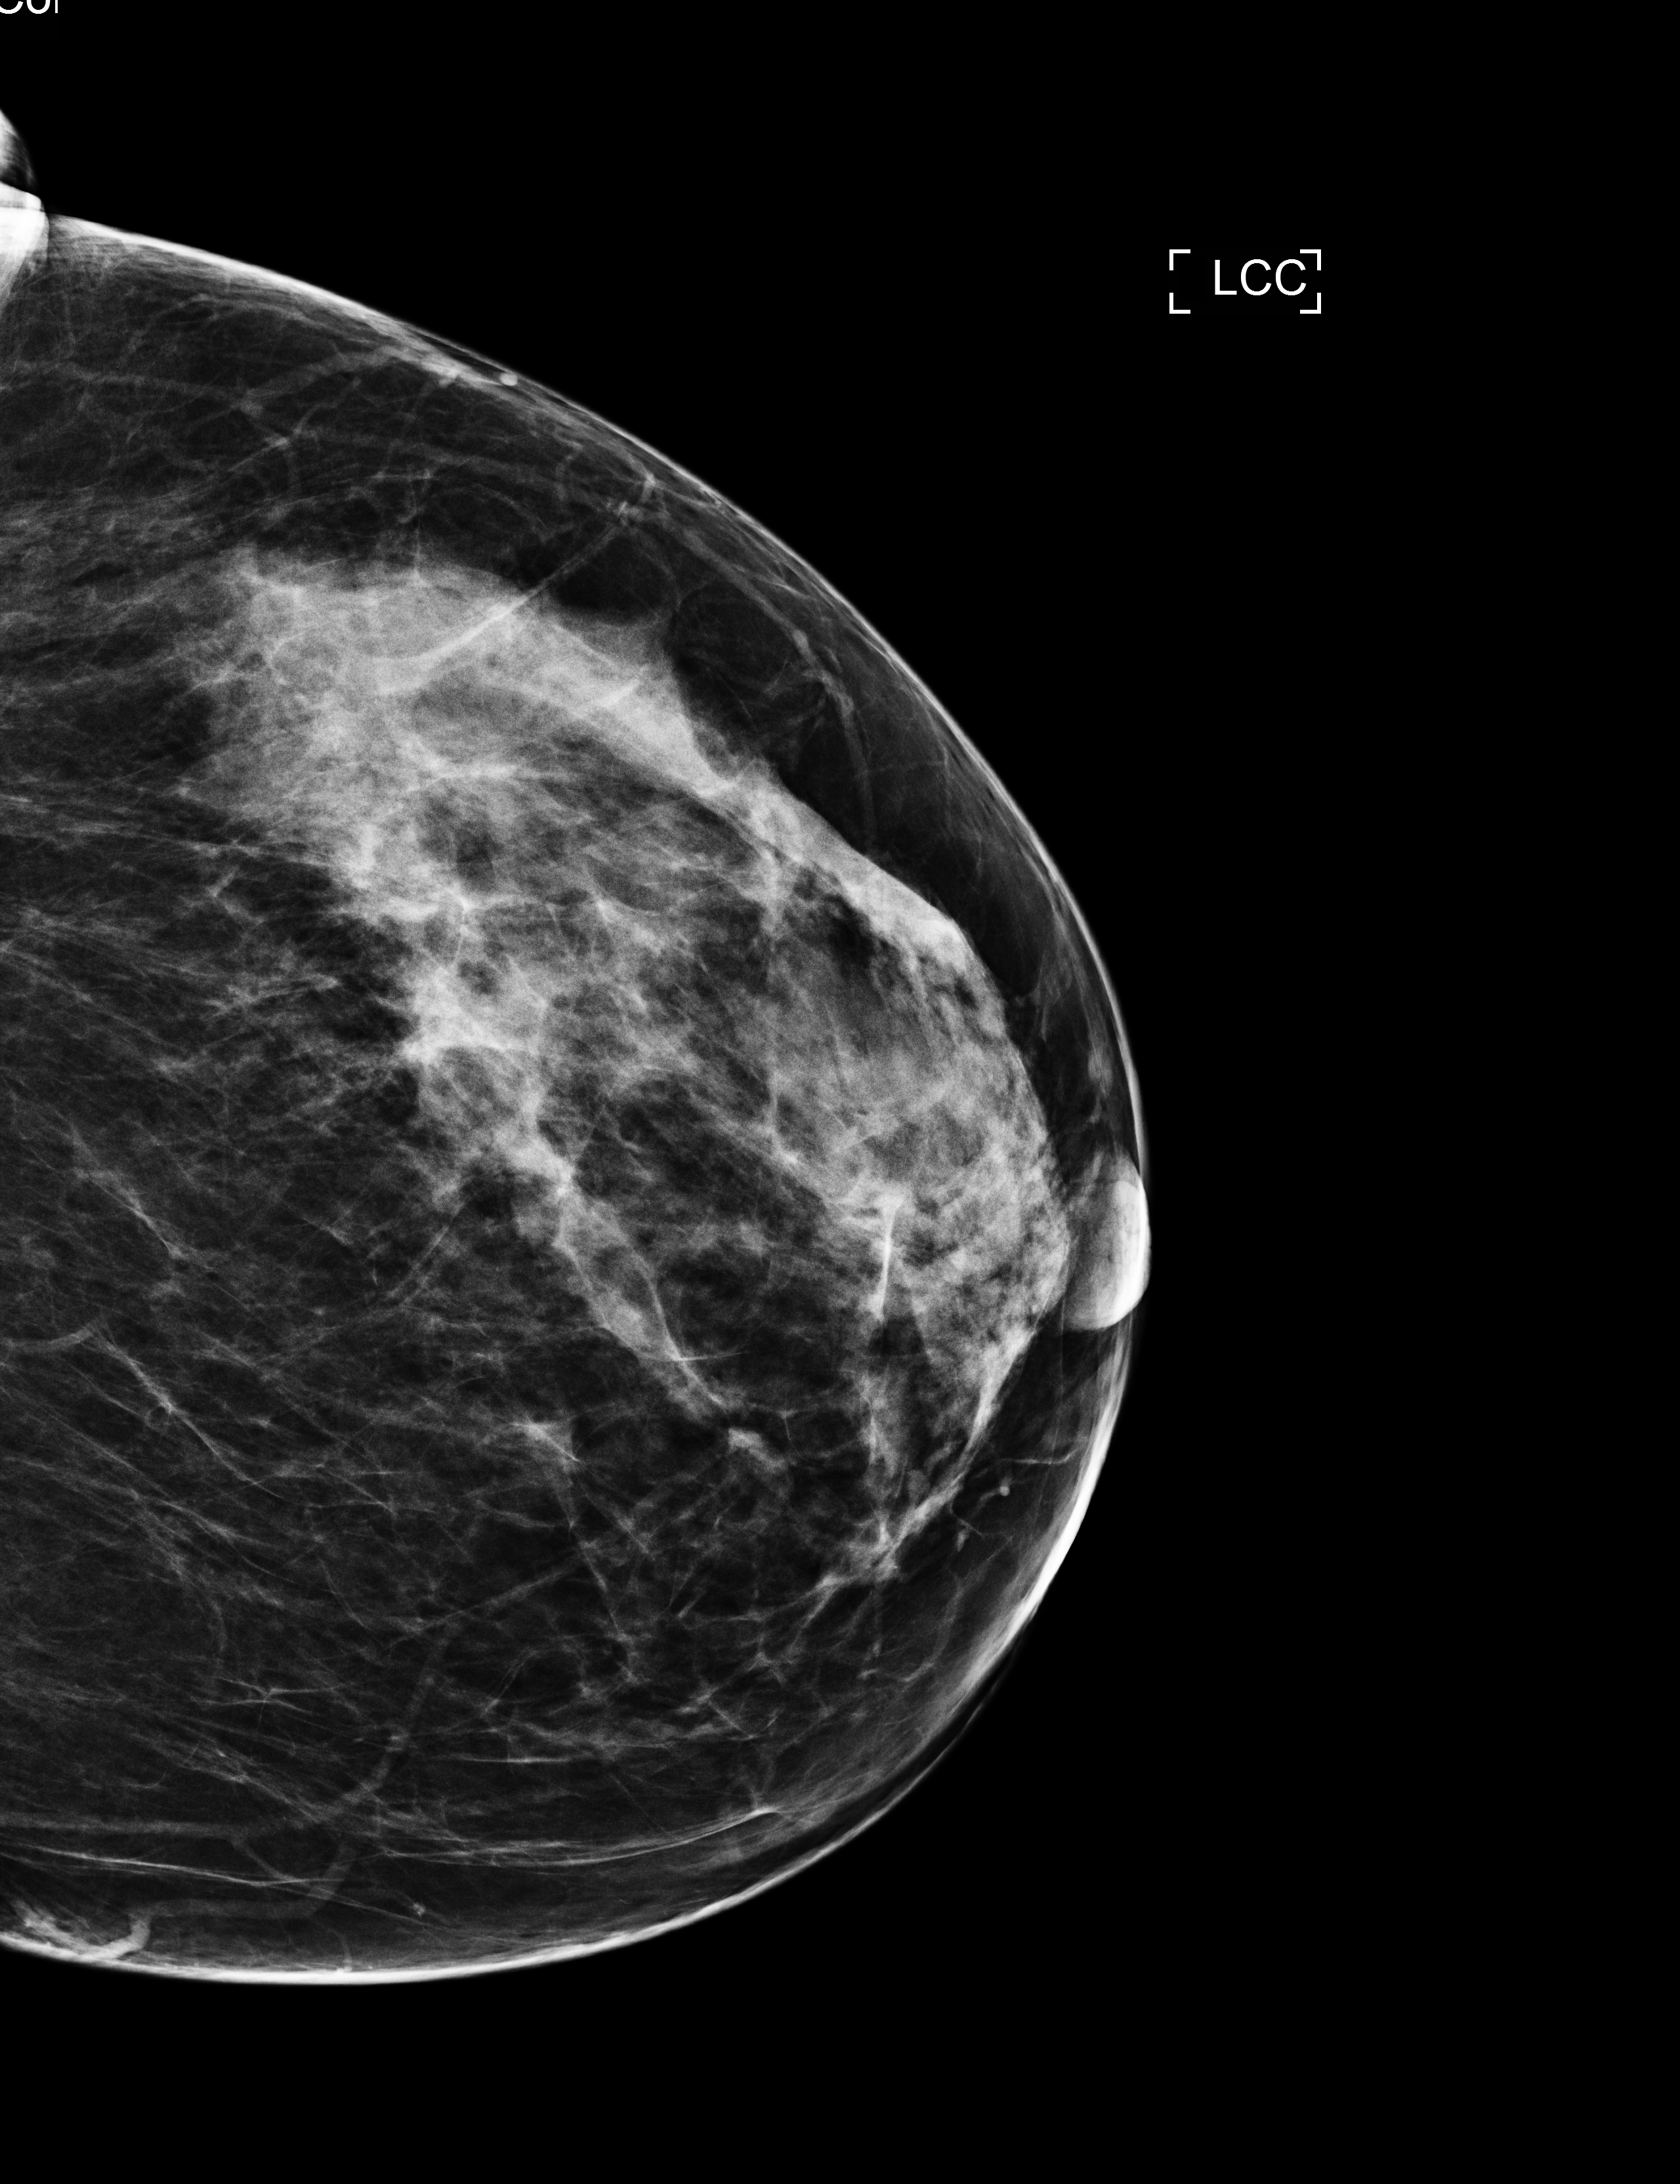
Full-field digital mammogram (FFDM), left breast, cranio-caudal projection, screening examination, compressed breast thickness 58 mm, system: Selenia Dimensions. Patient aged 41 years (female).
Breast density at the screening exam (both breasts): heterogeneously dense (BI-RADS density category c). Final BI-RADS category for the screening round (tomosynthesis exam, both breasts): category 1. Recall: recalled for additional imaging after this screen.